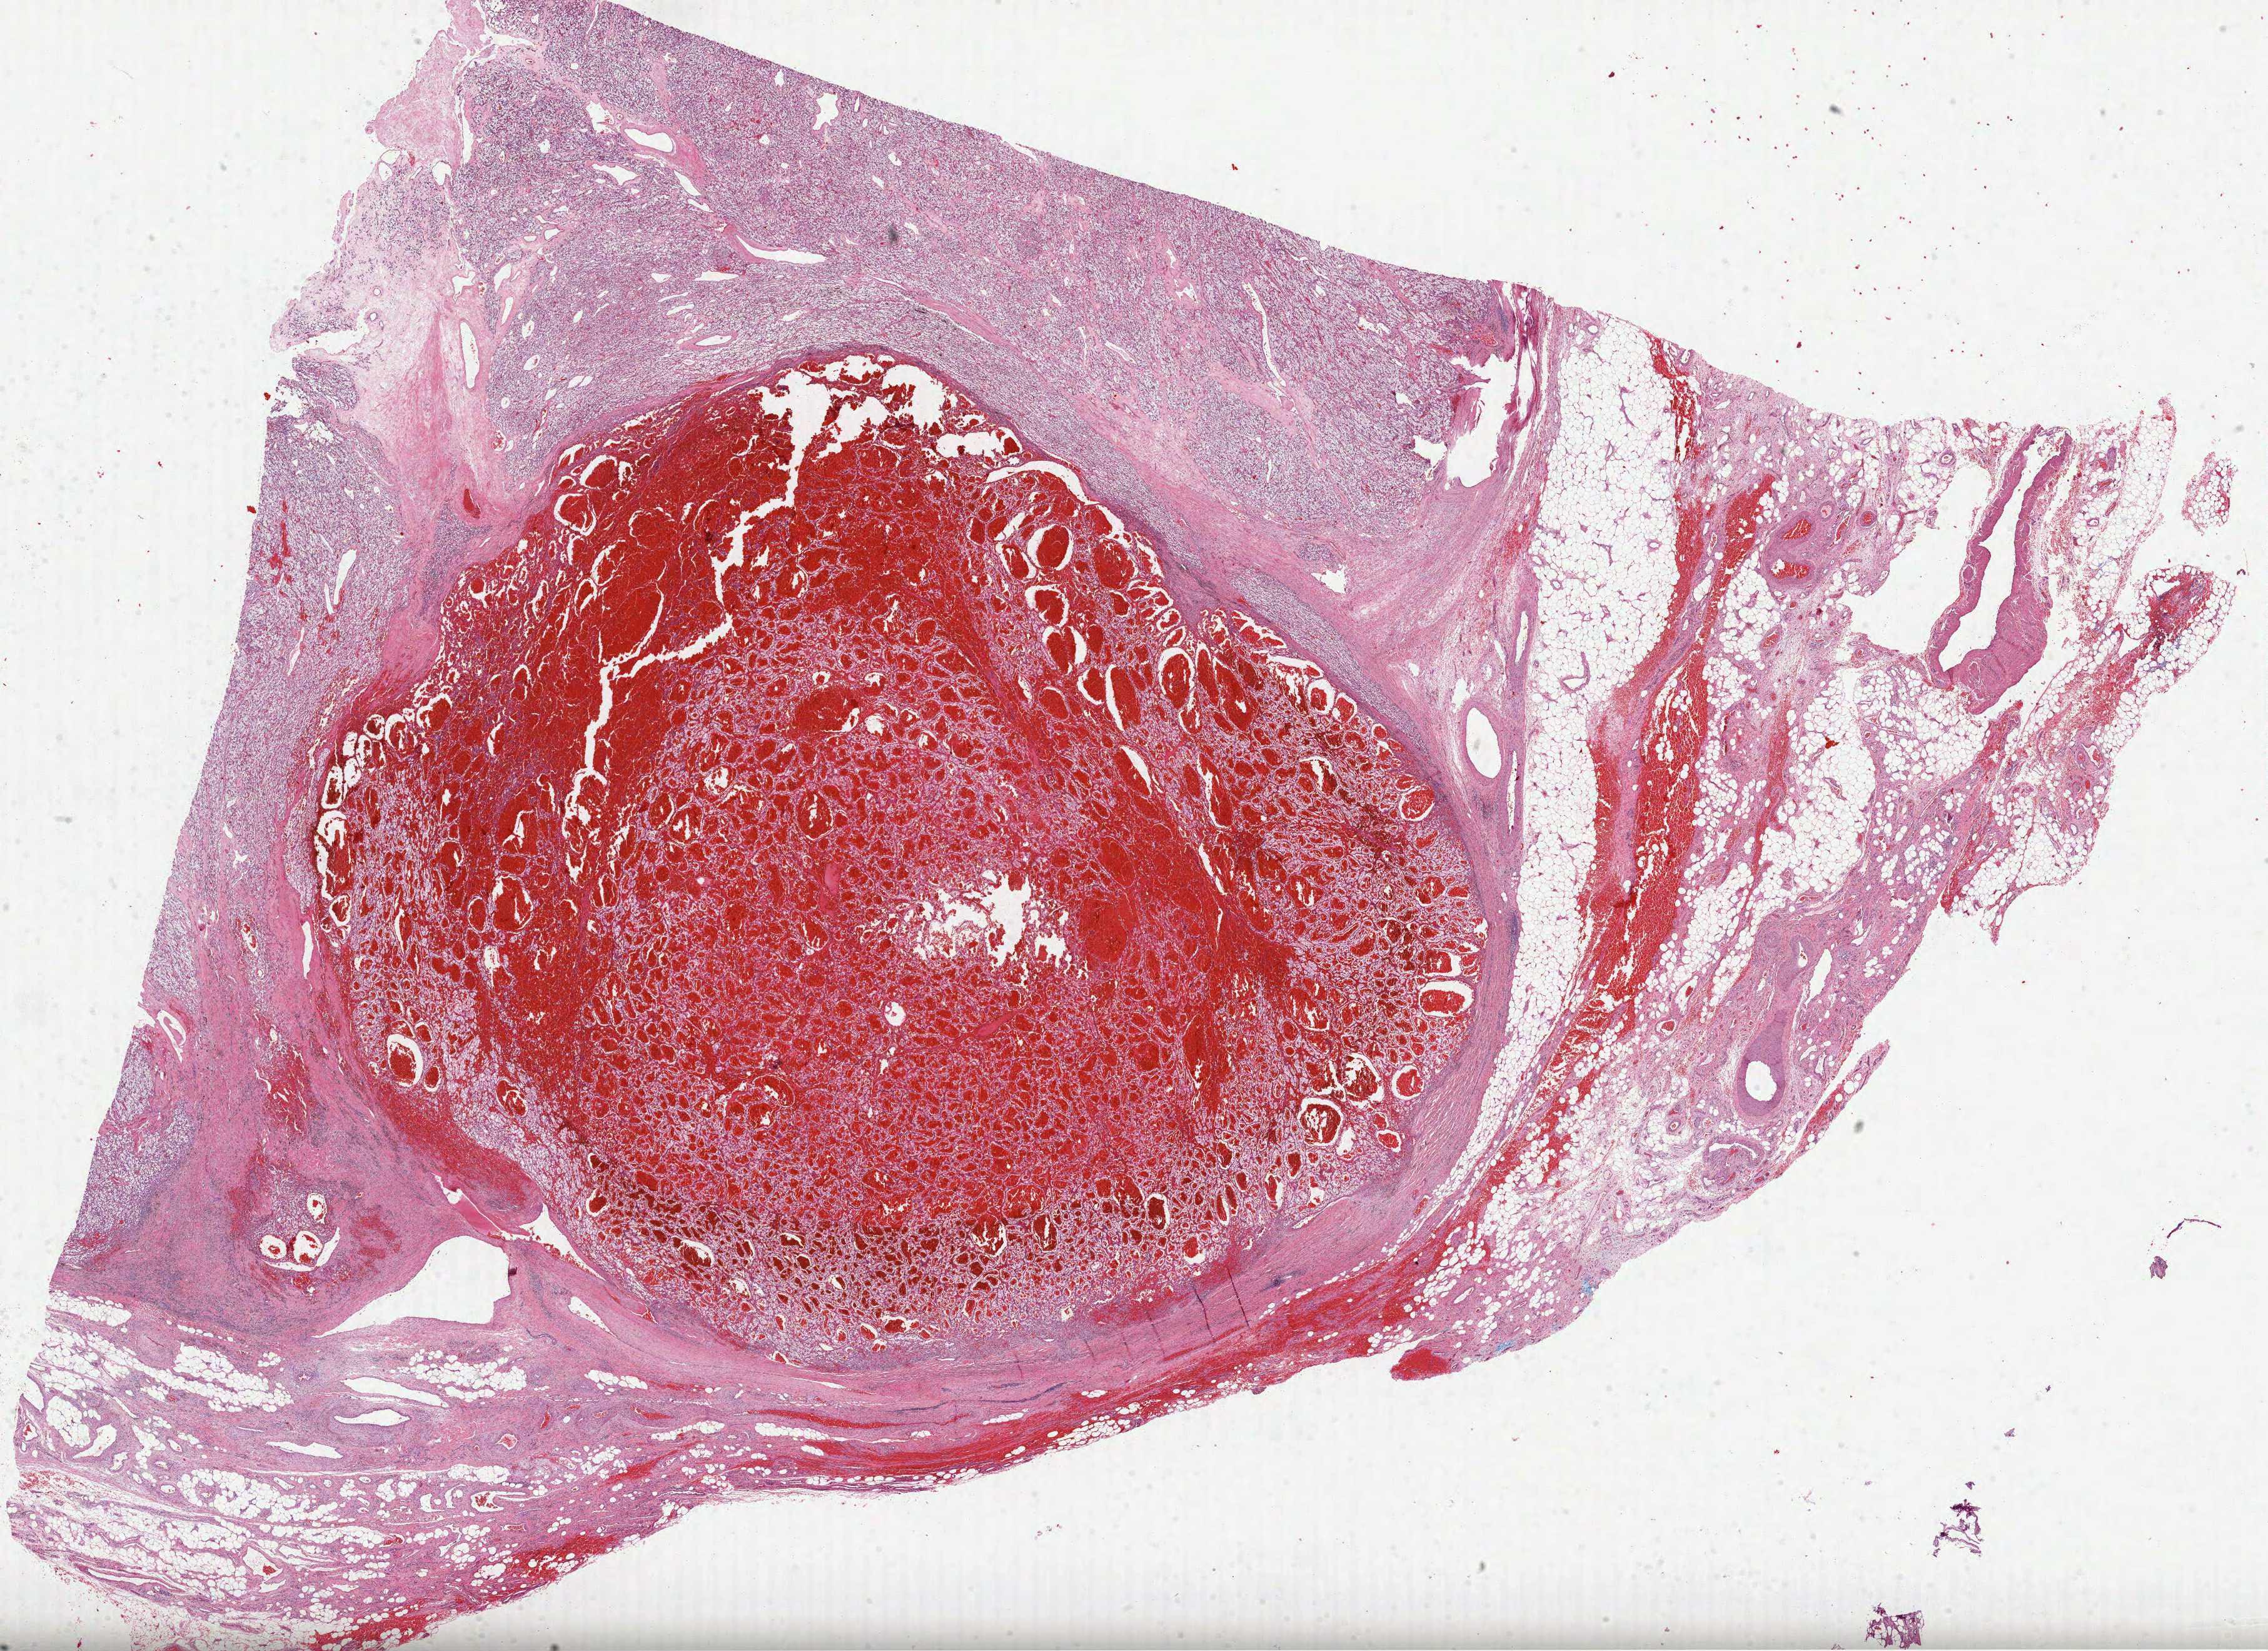
Digitized H&E-stained tissue section (whole slide) — shown as a low-resolution overview of the whole scanned area (about 29.2 x 21.3 mm), FFPE section, sample: primary tumour, kidney. Male, age 57 years at initial diagnosis. Histologic grade: G2 (moderately differentiated).
Pathologic diagnosis: Clear cell adenocarcinoma, NOS. AJCC pathologic stage: I (6th edition).